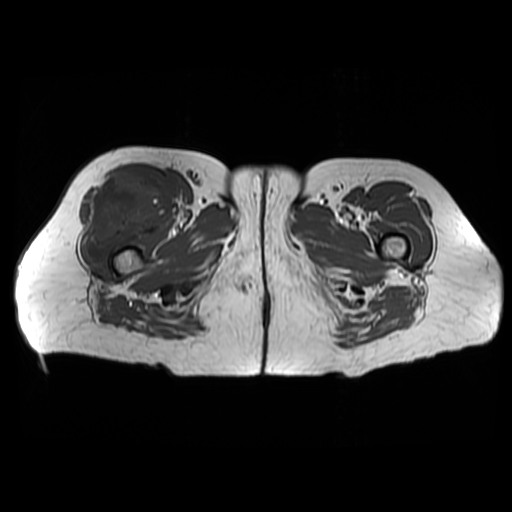
MRI of an extremity soft-tissue mass, one axial slice. Position 36 of 48 along the scan axis. 6 mm slice thickness. 512 × 512 image matrix, field of view 440 × 440 mm. Female patient. Case-level facts recorded for this patient, not image findings: histological type: pleiomorphic undifferentiated sarcoma; grade: high; site of the primary tumour: right quadricep.
Structures marked on this image (manually delineated by an expert):
- gross tumour volume including surrounding oedema: bounding box [x1, y1, x2, y2] px = [79, 172, 168, 259]
- gross tumour volume (mass): [79, 172, 168, 259]